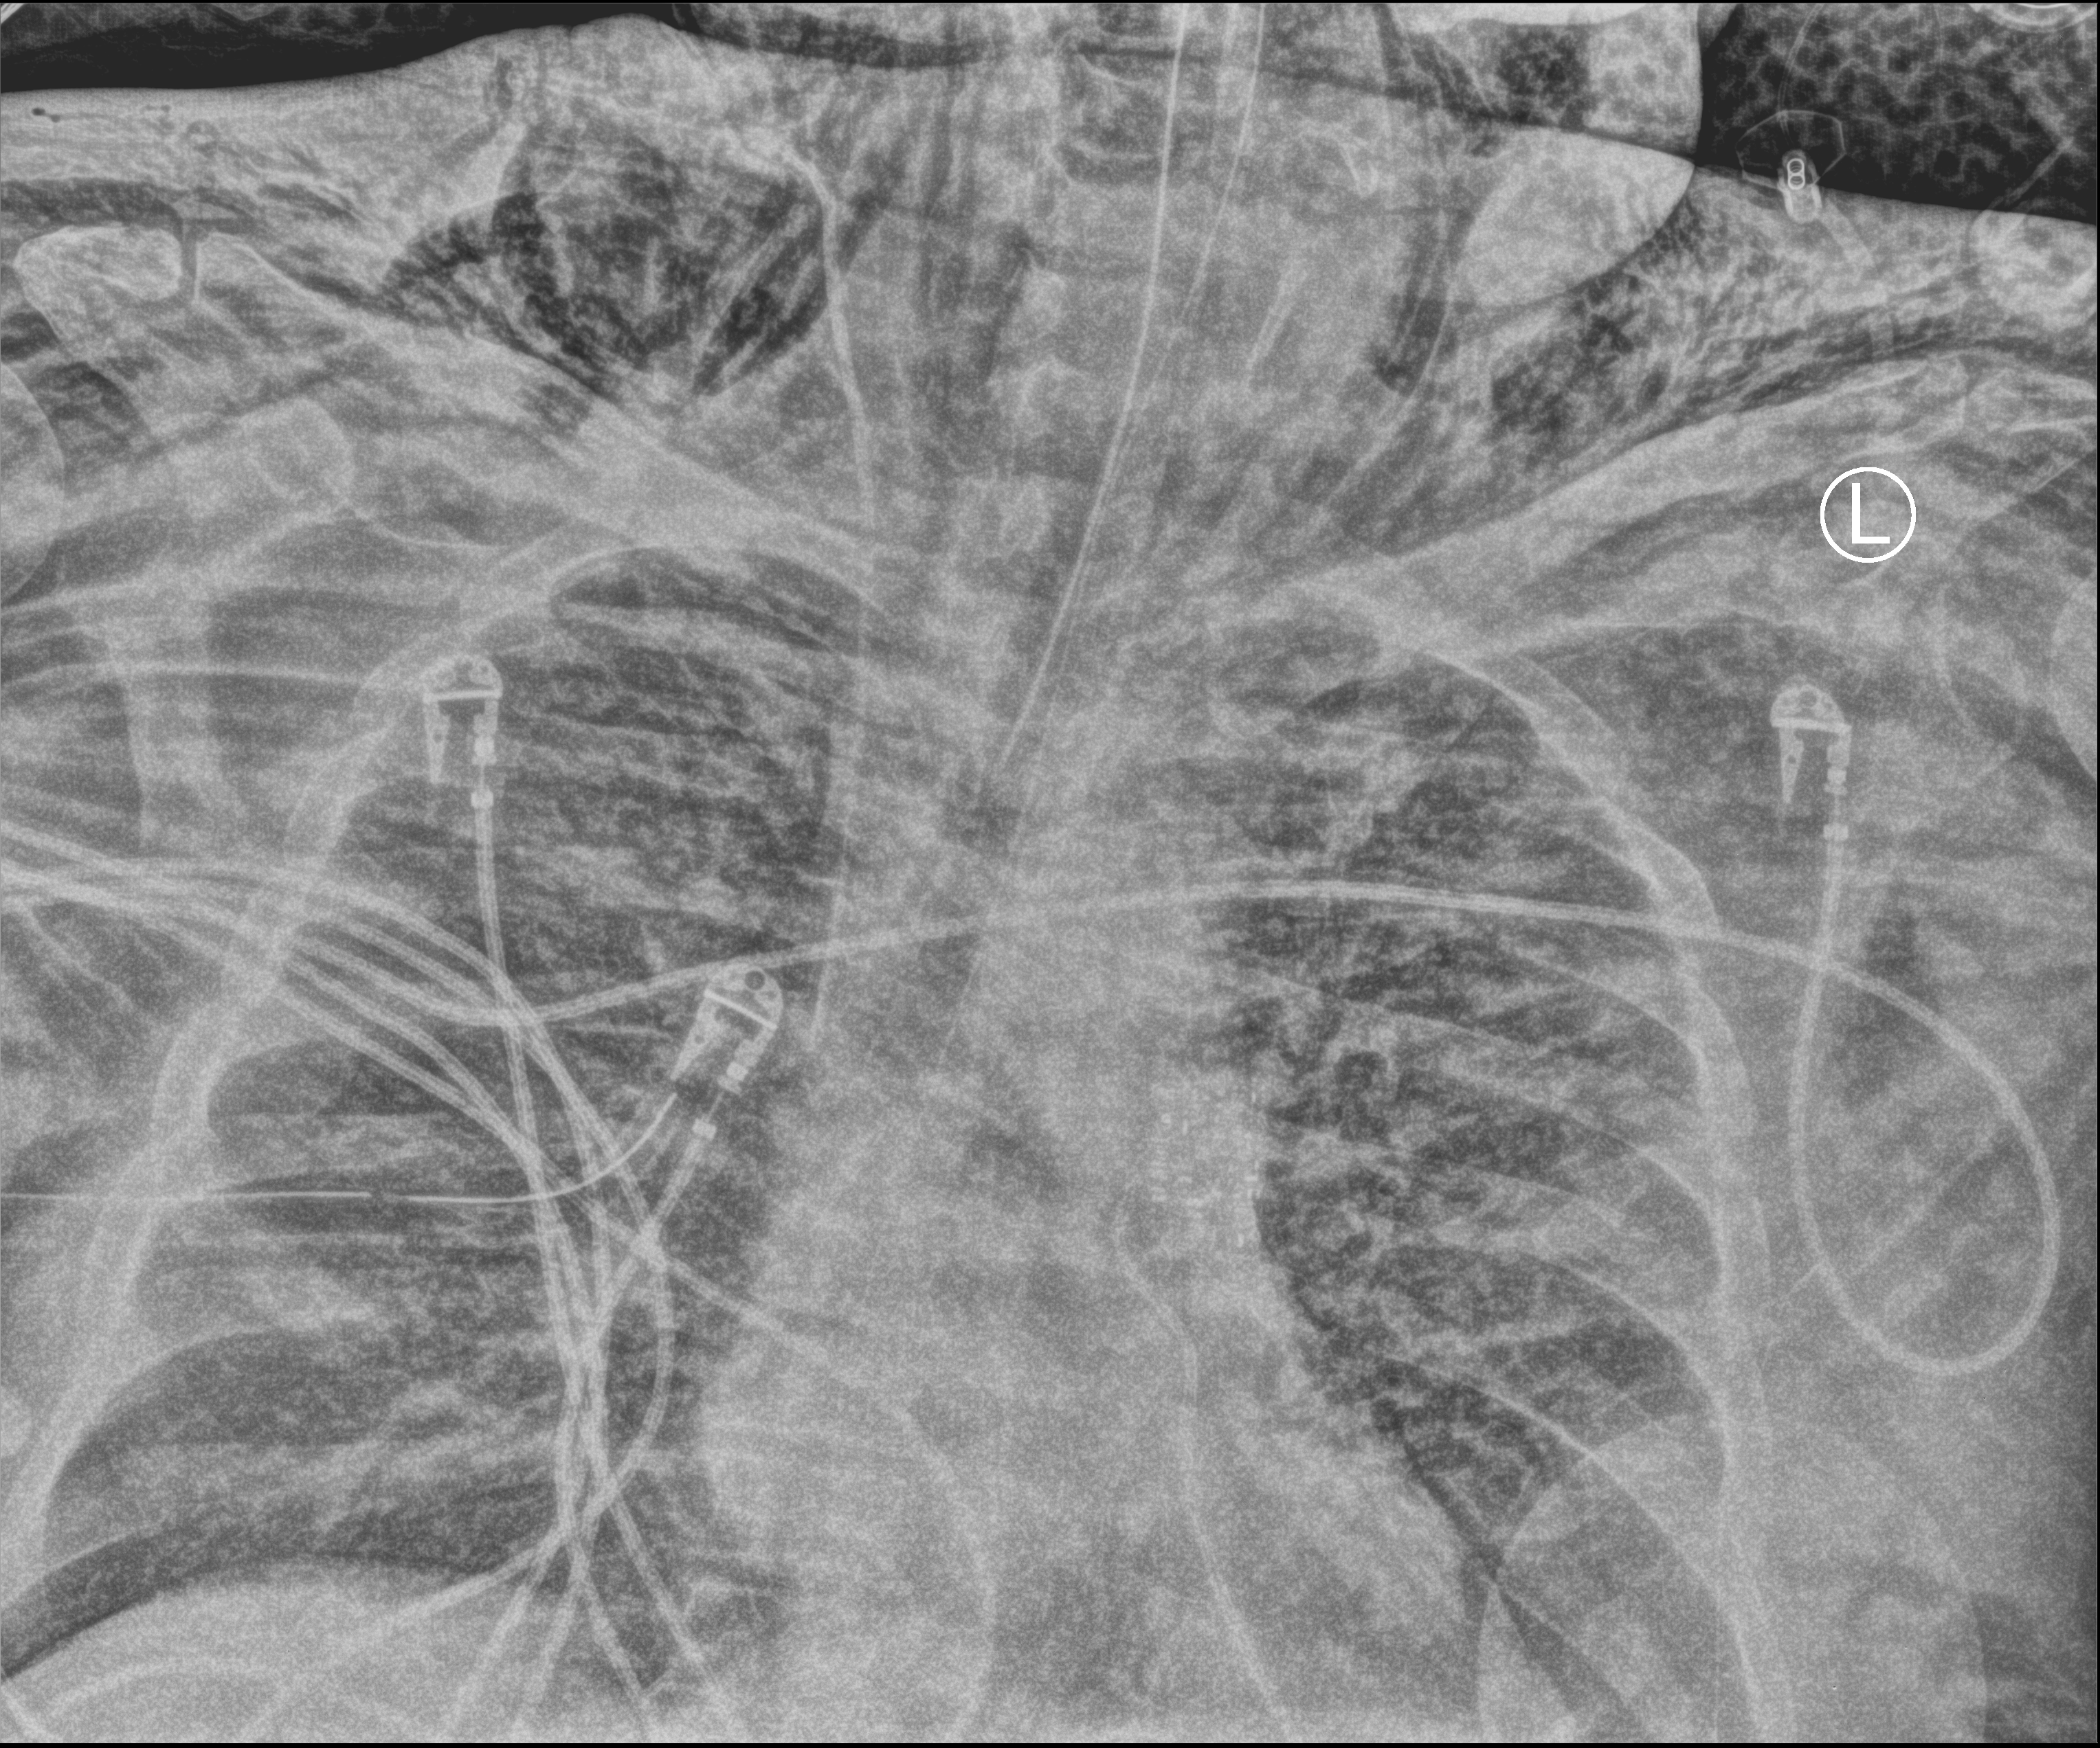
Chest X-ray (portable), anteroposterior (AP) projection. Patient hospitalised with COVID-19, aged 18–59 years.
Admission-level facts for this patient (not findings on this image; timing relative to this image not recorded): admitted to intensive care during this hospital stay: yes; mechanically ventilated during this hospital stay: yes.